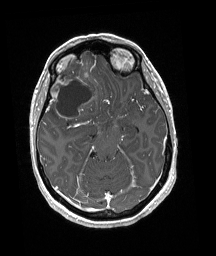
Brain MRI from a brain-tumour surgery series, one axial slice; position 117 of 192 along the scan axis; T1-weighted post-contrast; 1 mm slice thickness; 216 × 256 image matrix. Case-level facts recorded for this patient, not image findings: histopathology: Oligodendroglioma; WHO grade: 3; IDH mutation: yes; tumour location: Right Frontal.
Structures marked on this image (expert manual segmentation):
- tumour: box from (x=48, y=61) to (x=97, y=123) px